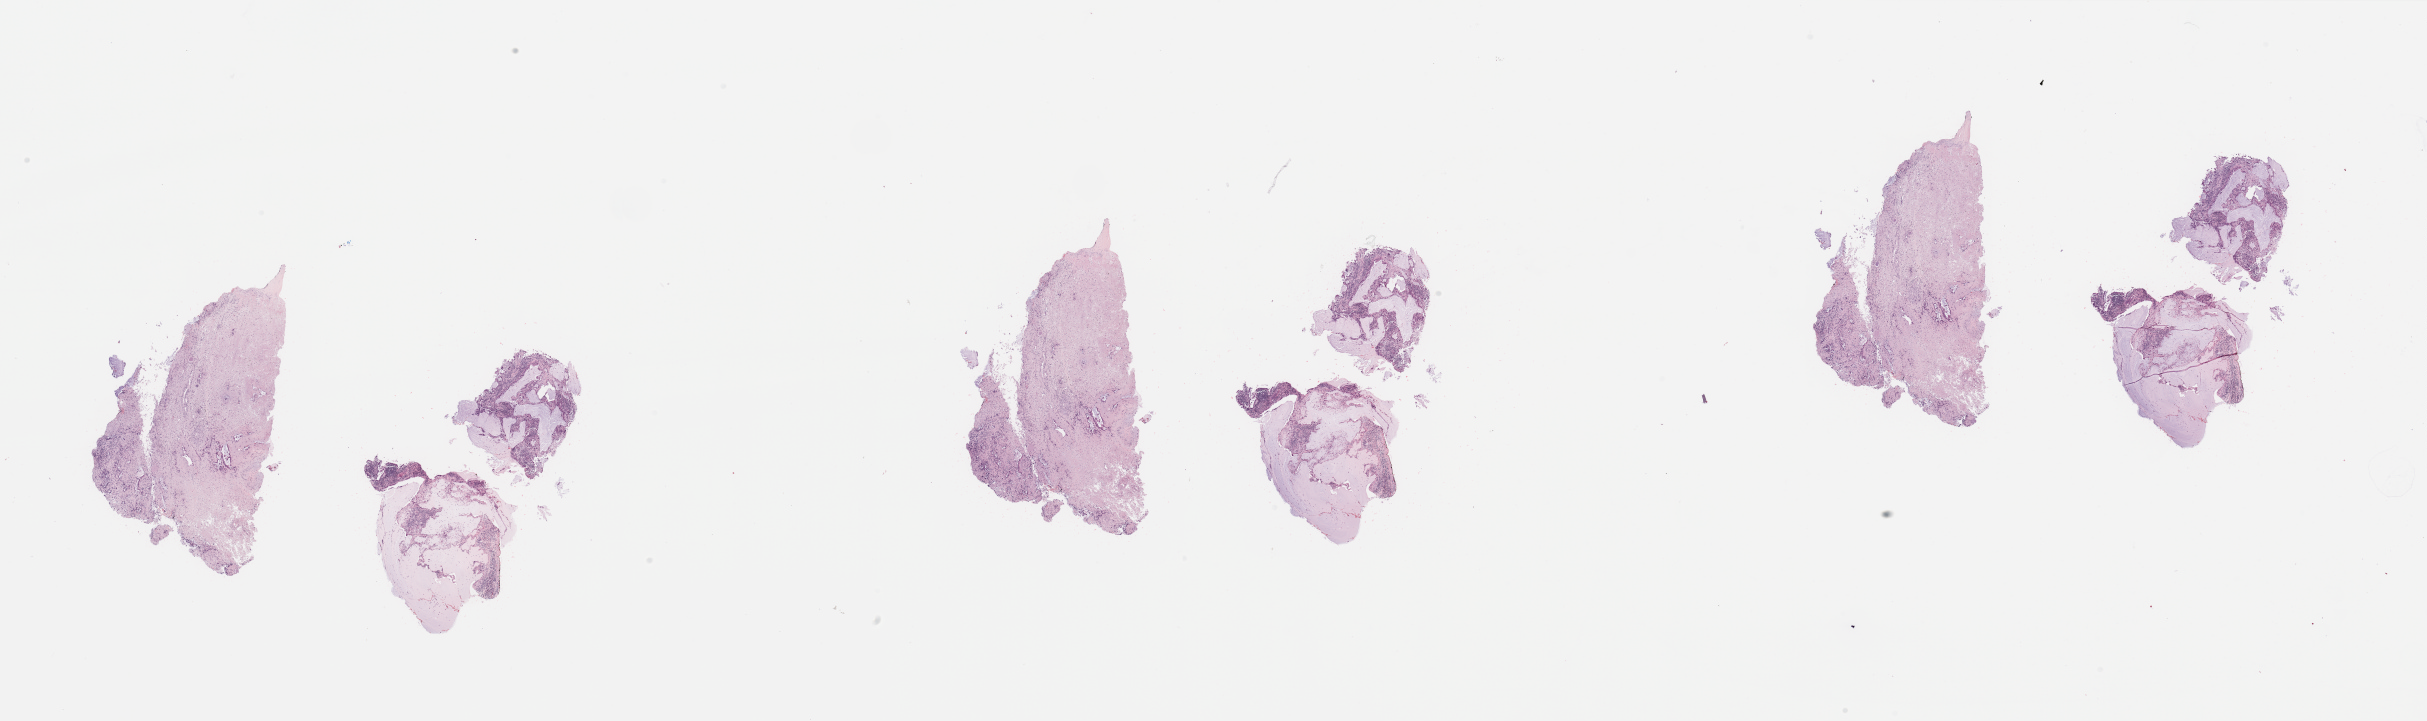
Whole-slide histology image, H&E-stained — a low-resolution overview of the entire scanned area, about 38.4 x 11.4 mm (acquisition: 20x scan), lung, tissue type not recorded.
* patient diagnosis (cohort enrolment): lung adenocarcinoma (lung)